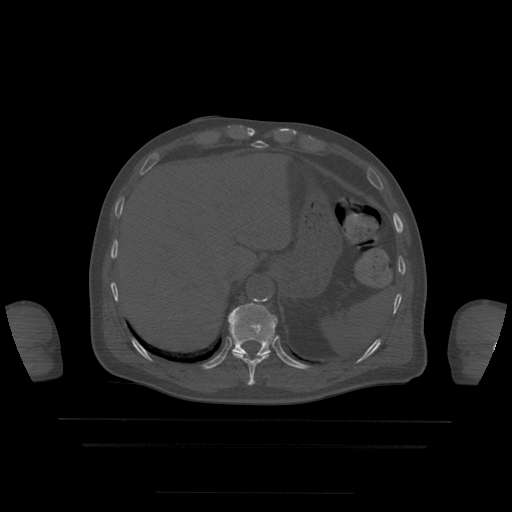
CT including the spine, one axial slice. Position 230 of 522 along the scan axis. Bone window (W 1800 / L 400 HU). 1.25 mm slice thickness. 512 × 512 image matrix, field of view 436 × 436 mm. Patient age 68 years. Case-level facts recorded for this patient, not image findings: primary cancer: urothelial.
Annotated regions visible in this slice (semi-automatic segmentation, software-assisted and operator-edited):
- T10 vertebra: bounding box [x1, y1, x2, y2] px = [232, 351, 269, 386]
- T11 vertebra: [228, 303, 278, 356]